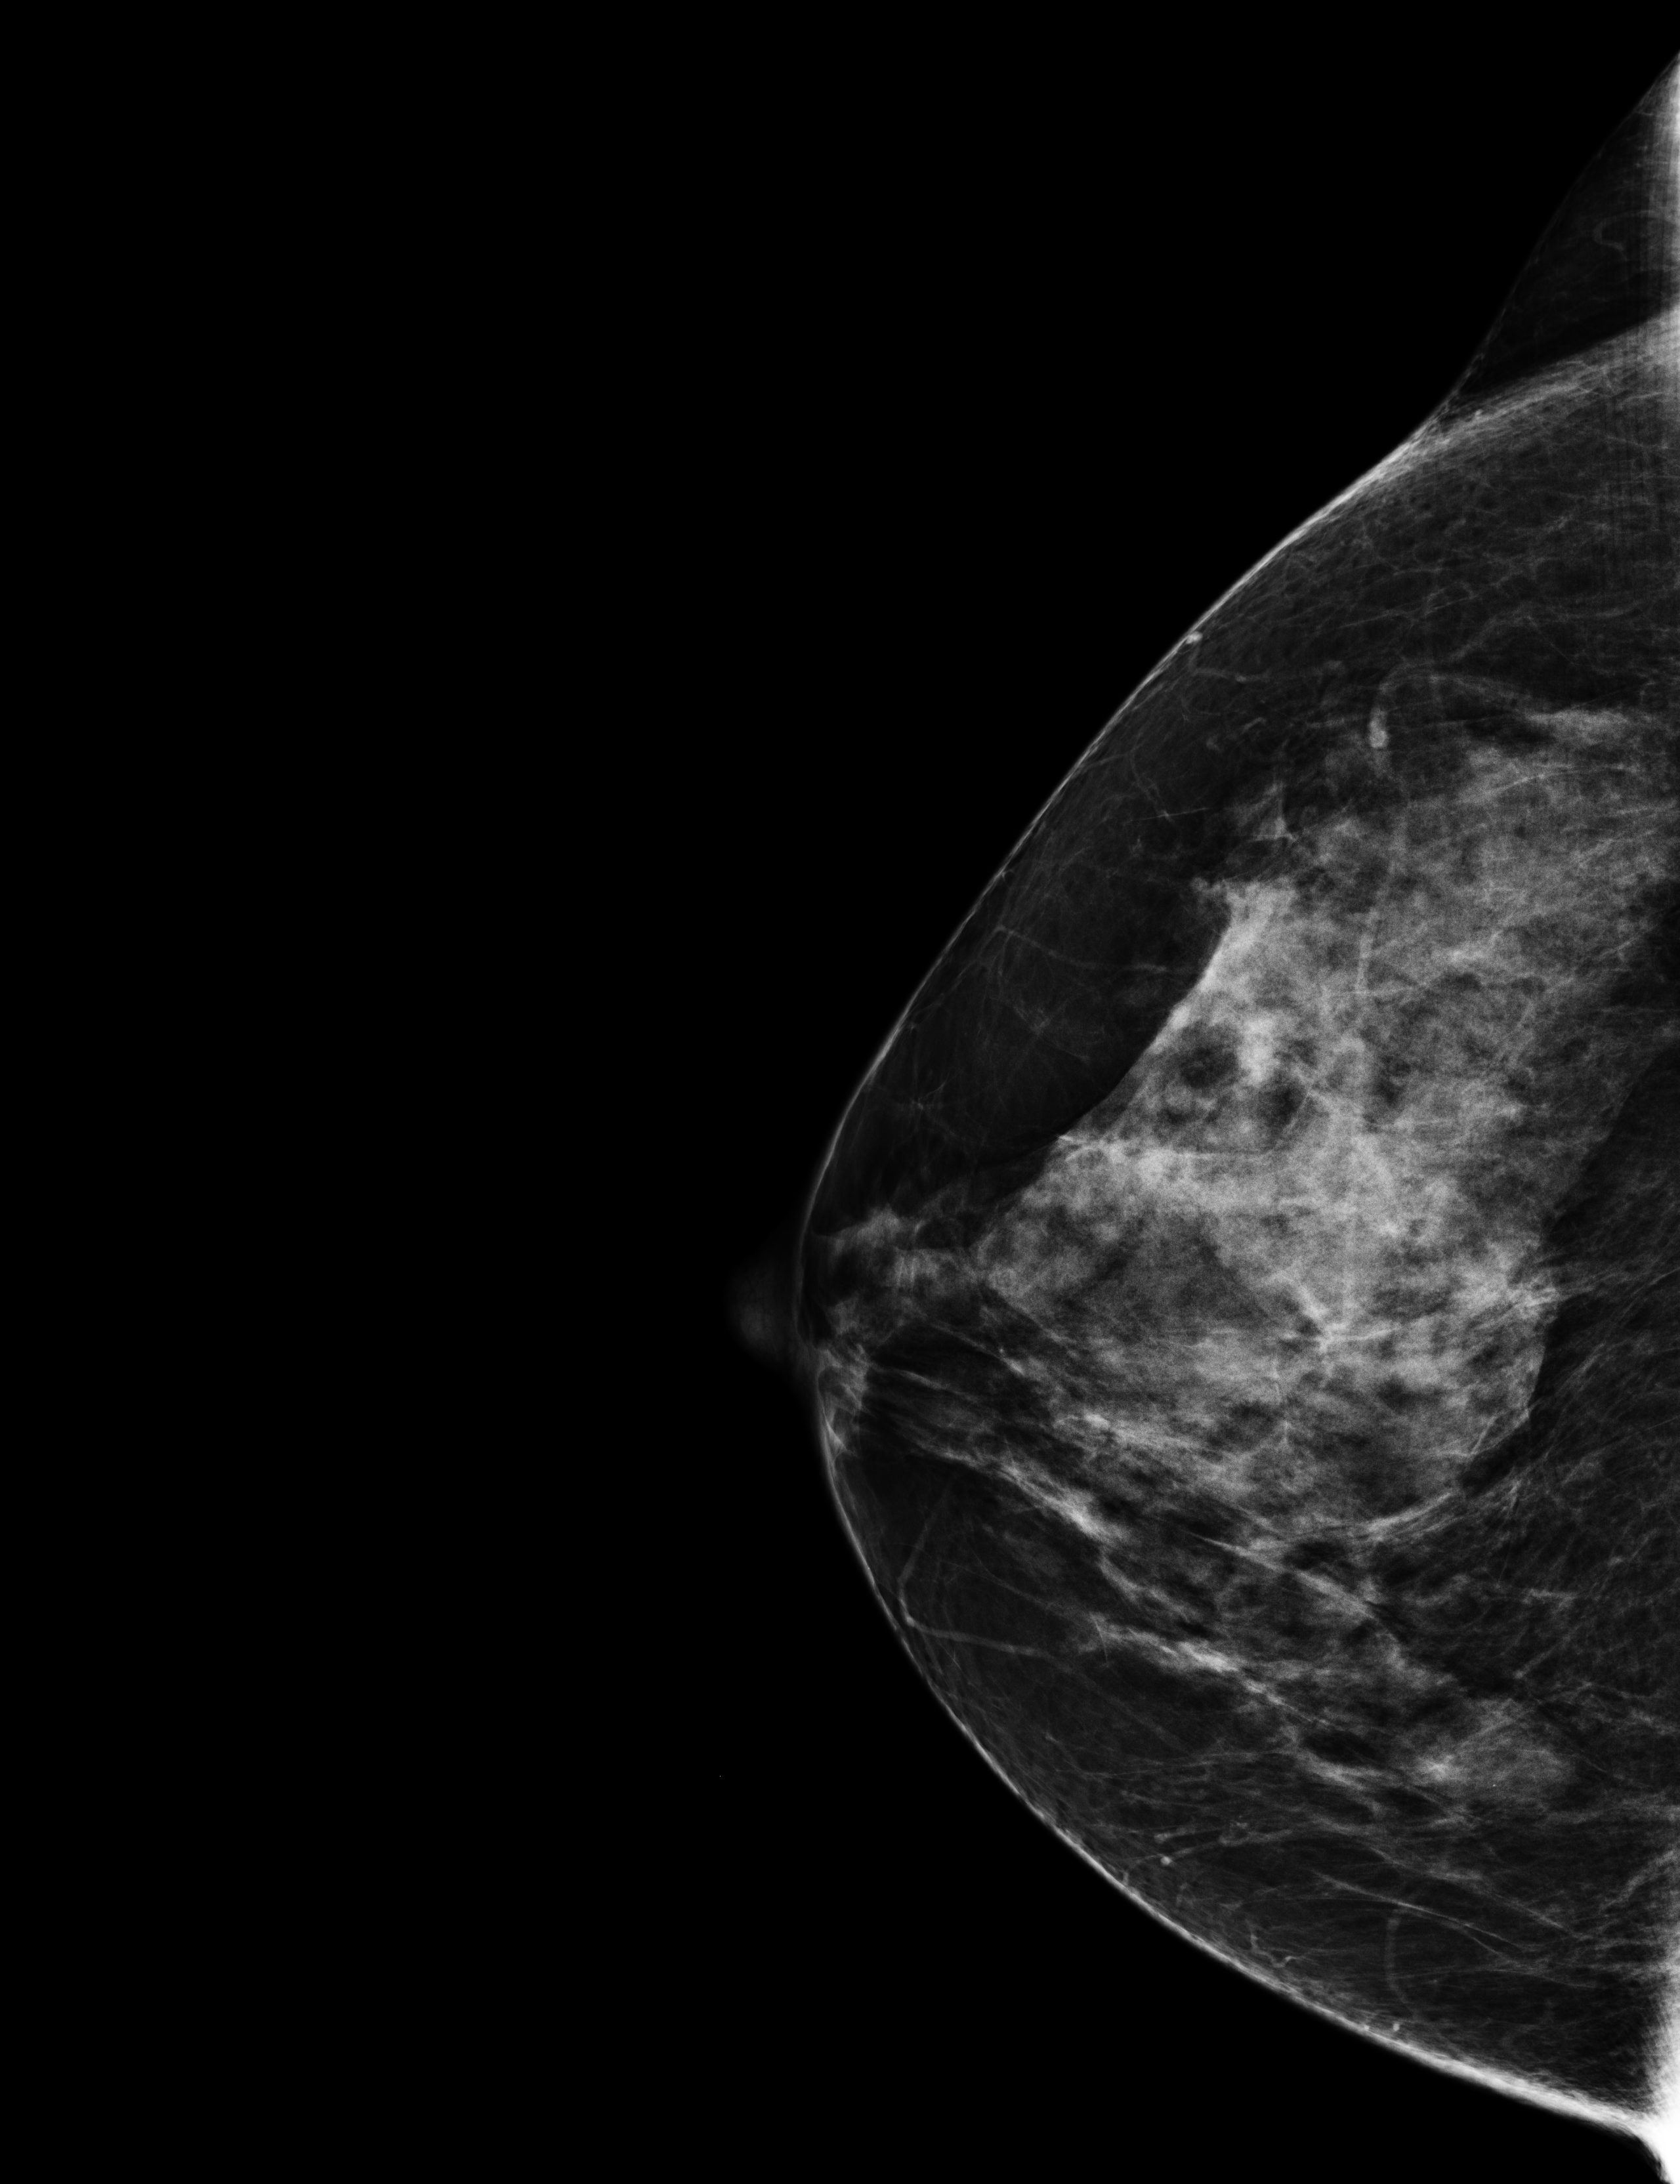
Screening examination; compressed breast thickness 73 mm. Patient: female, 51 years.
Image type: full-field digital mammogram. Breast: right. Projection: cranio-caudal projection.